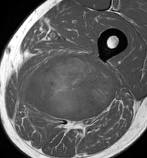
MRI of an extremity soft-tissue mass, one axial slice. Position 63 of 86 along the scan axis. MR volume resampled by the dataset authors to the PET/CT grid (not the native acquisition matrix). 3.27 mm slice thickness. 147 × 158 image matrix, field of view 144 × 154 mm. Male patient. Case-level facts recorded for this patient, not image findings: histological type: undifferentiated pleomorphic liposarcoma; grade: high; site of the primary tumour: left thigh.
Outlined on this slice (expert contour drawn on MRI and transferred to this co-registered scan by the dataset authors):
- gross tumour volume including surrounding oedema: bounding box <16,53,115,130> (left, top, right, bottom; pixels)
- gross tumour volume (mass): <23,53,115,120>